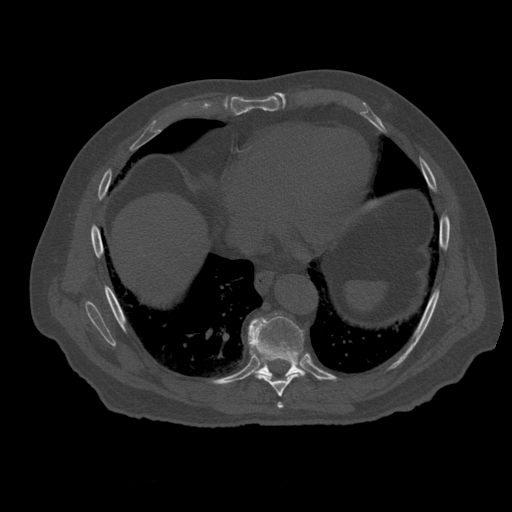
CT including the spine, one axial slice; position 331 of 399 along the scan axis; reconstruction kernel STANDARD; bone window (W 1800 / L 400 HU); 1.25 mm slice thickness; 512 × 512 image matrix, field of view 407 × 407 mm. Patient age 73 years. Case-level facts recorded for this patient, not image findings: primary cancer: prostate.
Outlined on this slice (semi-automatically segmented with operator editing):
- T7 vertebra: bounding box (x1, y1, x2, y2) in pixels: (278, 402, 283, 409)
- T8 vertebra: (257, 374, 302, 397)
- T9 vertebra: (249, 315, 306, 378)